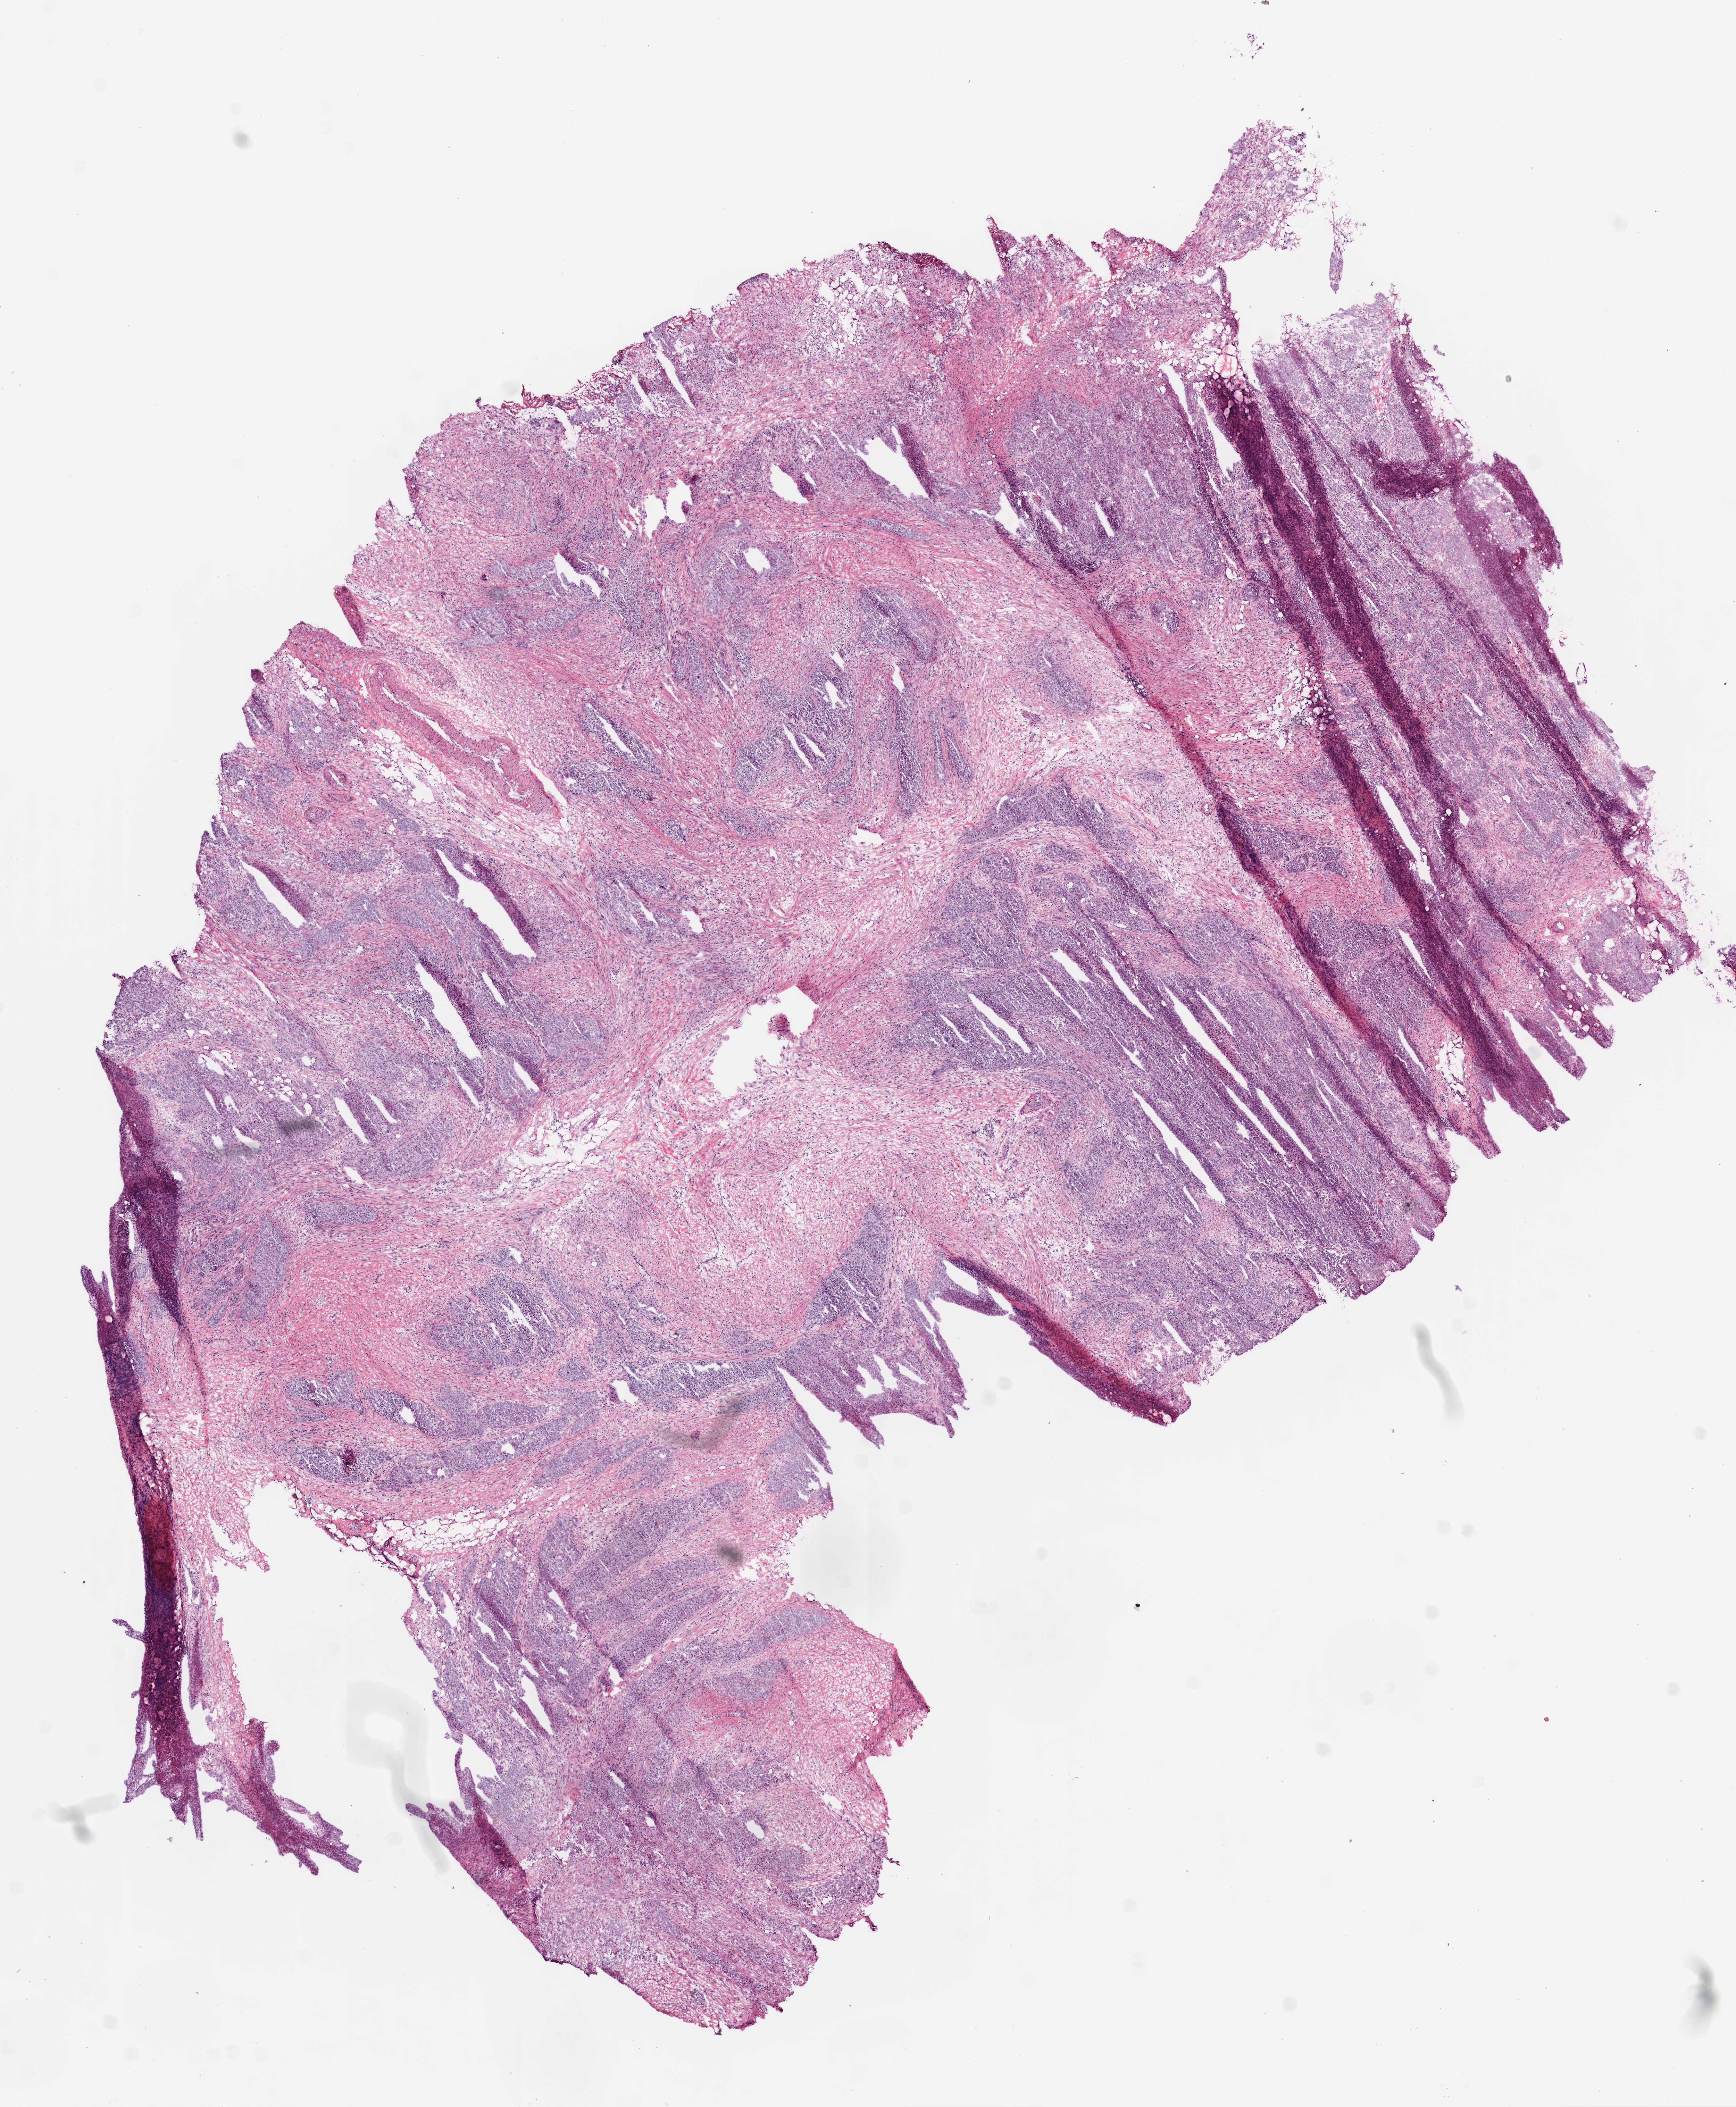
Whole-slide histology image, Hematoxylin and eosin (H&E) stained — a low-resolution overview of the entire scanned area, about 10.0 x 12.2 mm (from a 20x scan). Composition of this section per pathologist review: tumour cells 57%, tumour nuclei 65%, normal cells 0%, stromal cells 40%, necrosis 3%.
• specimen: frozen section from the bottom of the tissue portion; sample: primary tumour, ovary